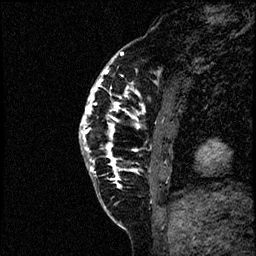
Breast MRI (dynamic contrast-enhanced), one sagittal slice. Position 17 of 60 along the scan axis. Dynamic contrast-enhanced study with each time point stored as its own series, time point 2 of 4 at this slice position (early post-contrast, ordered by acquisition time). 1.5 T. TE 4.2 ms, TR 17.6 ms. 2 mm slice thickness. 256 × 256 image matrix, field of view 200 × 200 mm. Female patient, age 40 years. From the clinical record (not read from this slice): setting: breast cancer imaged before/during neoadjuvant chemotherapy; receptor status: HER2-positive.
Structures marked on this image (semi-automatic segmentation, software-assisted and operator-edited):
- analysis volume of interest (the breast-tissue region the enhancement analysis was run in; not a lesion): bounding box [x1, y1, x2, y2] px = [80, 56, 197, 205]
- tumour enhancement mask (voxels above the 100 % enhancement threshold inside the analysis volume of interest): [80, 66, 146, 186]